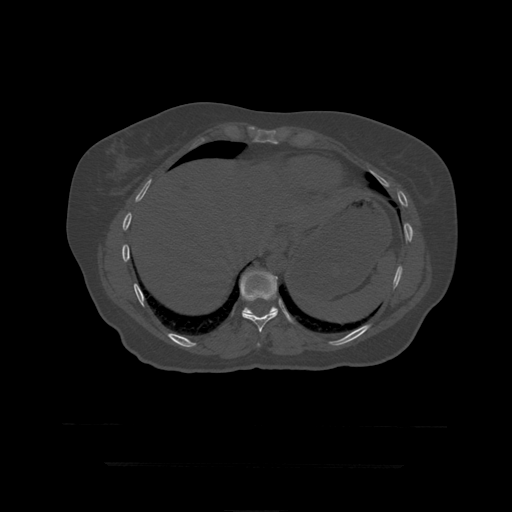
CT including the spine, one axial slice. Position 236 of 399 along the scan axis. Reconstruction kernel STANDARD. 120 kVp. Bone window (W 1800 / L 400 HU). 512 × 512 image matrix. Patient age 41 years. From the clinical record (not read from this slice): primary cancer: breast.
Outlined on this slice (semi-automatic segmentation, software-assisted and operator-edited):
- T10 vertebra: bounding box (x1, y1, x2, y2) in pixels: (241, 271, 278, 333)
- T11 vertebra: (240, 270, 279, 315)
- T9 vertebra: (257, 343, 260, 347)